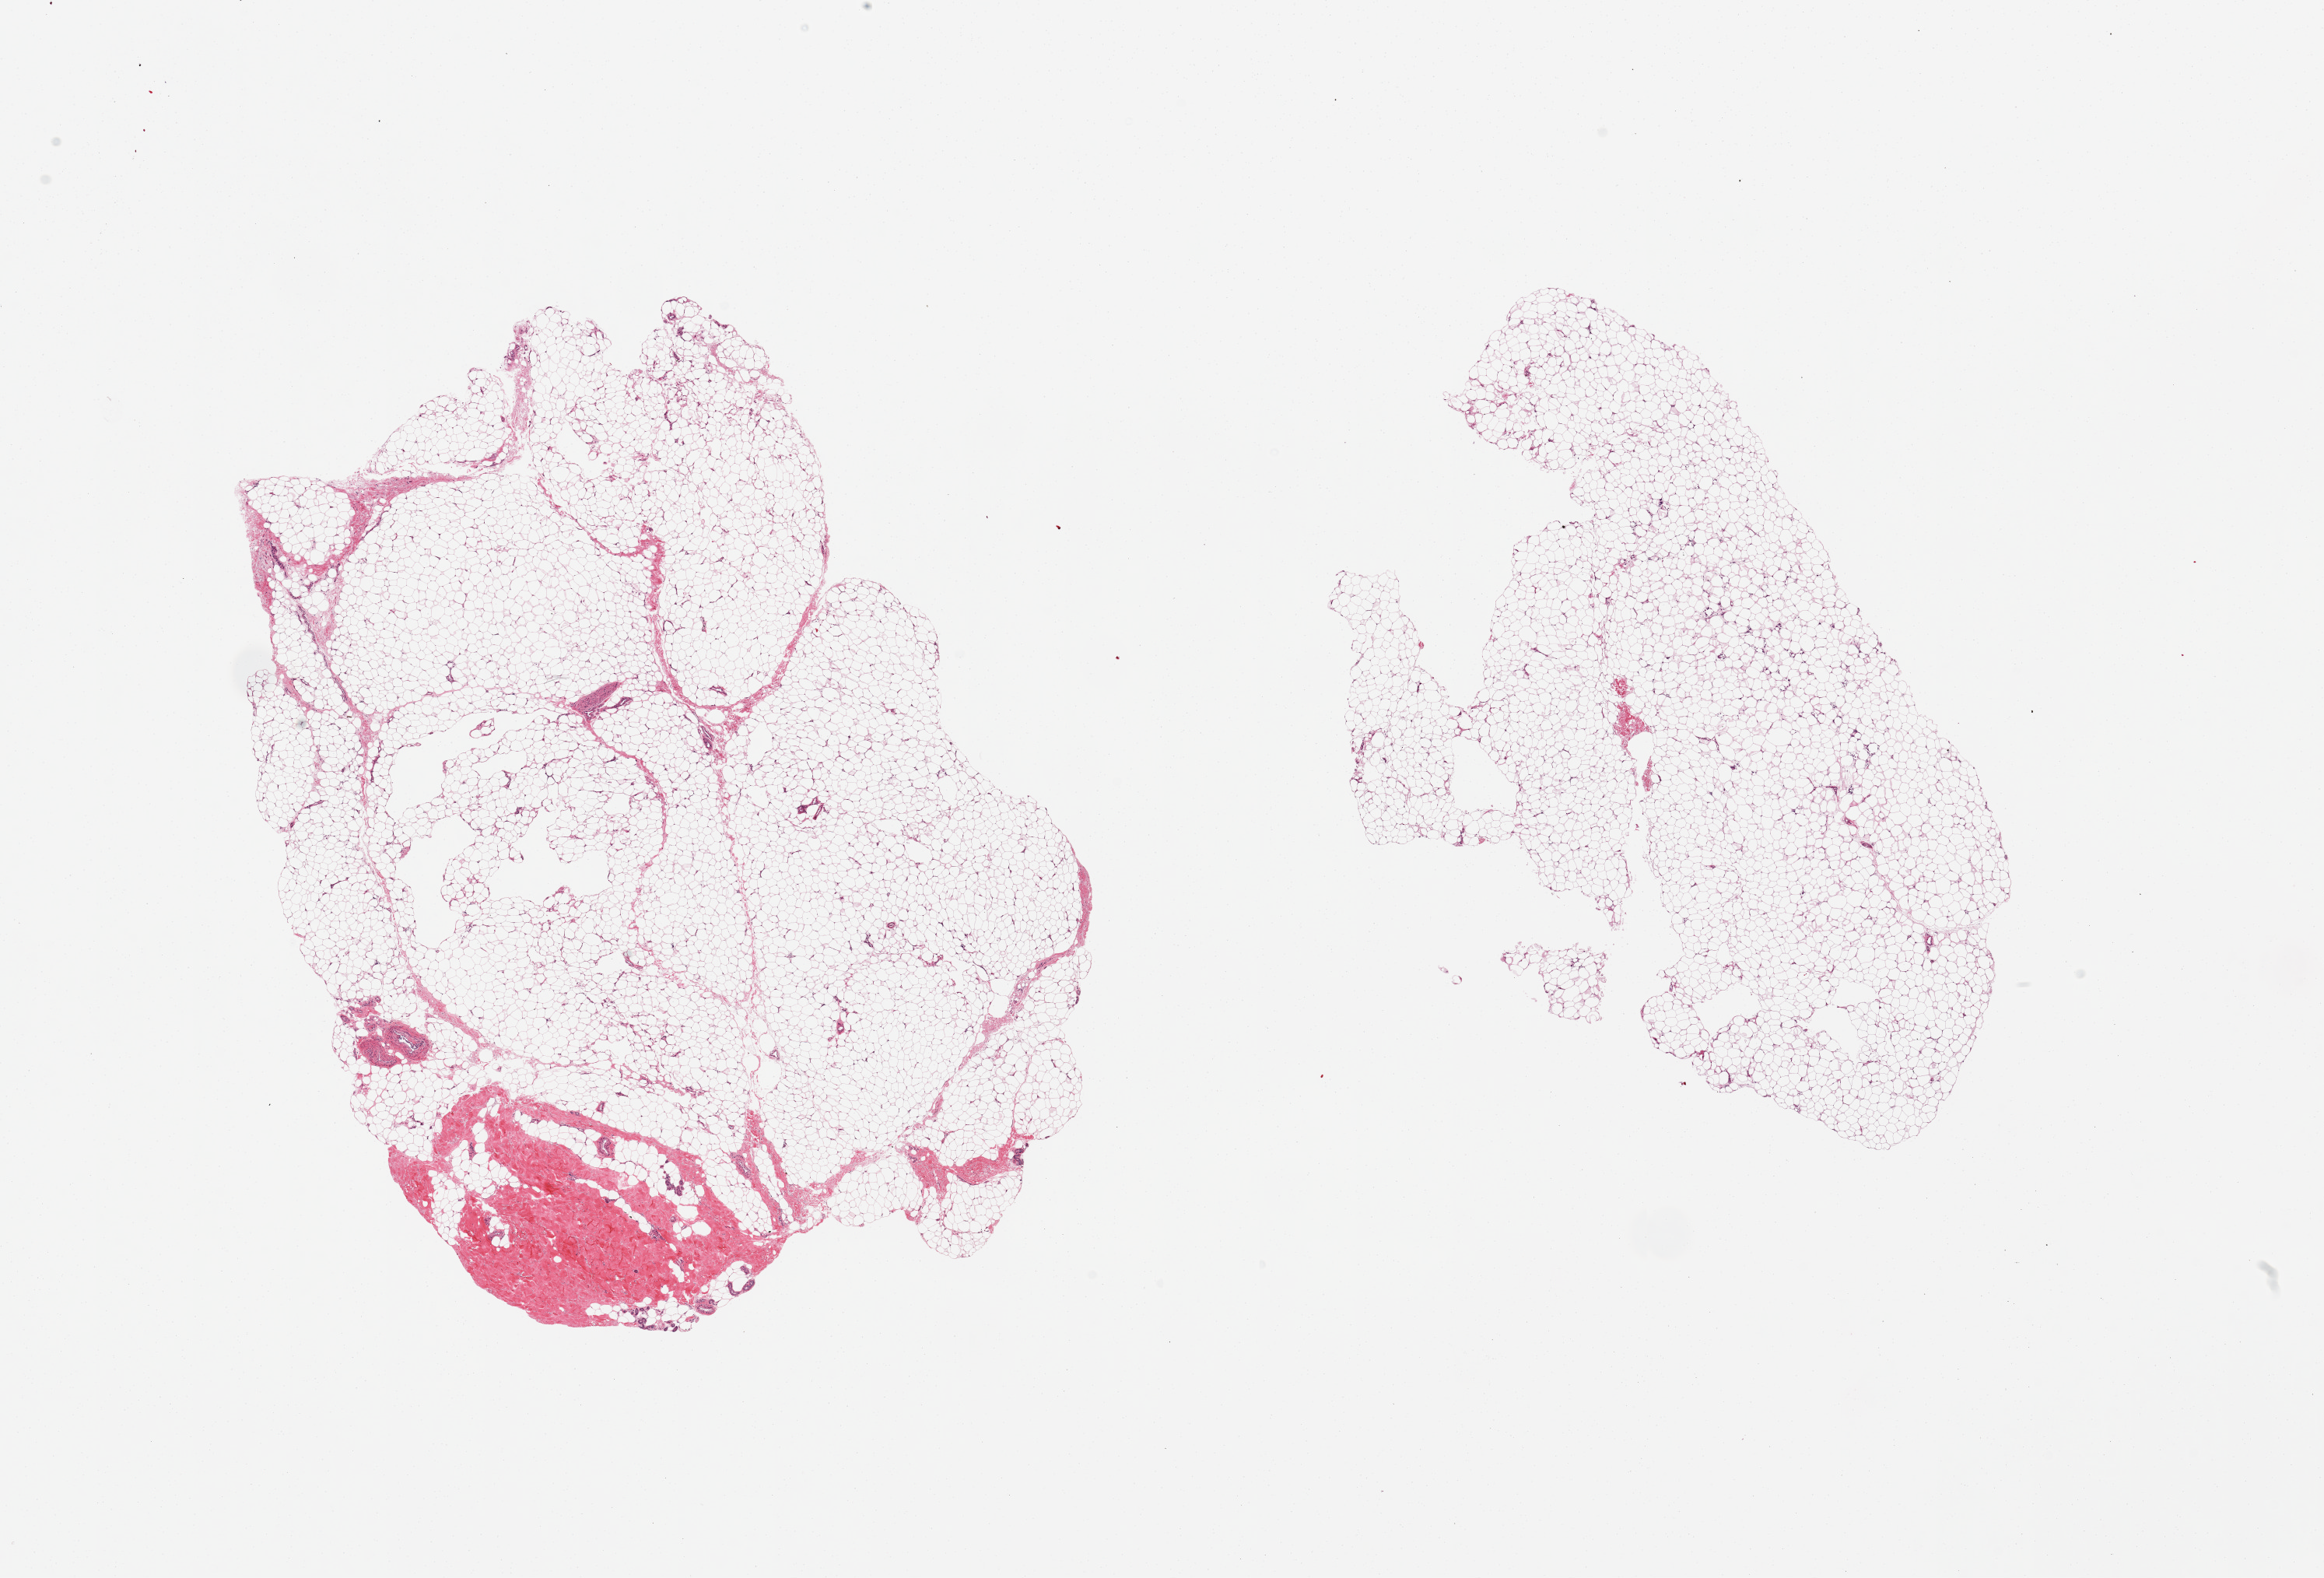
Whole-slide image, haematoxylin and eosin stain — a low-resolution overview of the entire scanned area, about 23.6 x 16.0 mm, PAXgene-fixed paraffin-embedded (PFPE) section, sampled site (target tissue): adipose tissue, tissue donor sample. Female donor.
Reviewer comment on this tissue sample: 2 pieces: 4 x 2mm of dermis present.